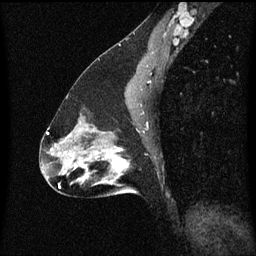
Breast MRI (dynamic contrast-enhanced), one sagittal slice; slice 34 of 60 in the series (ordered by position); dynamic contrast-enhanced series, image 2 of 3 at this slice position (ordered by acquisition); 1.5 T; TE 4.2 ms, TR 8.4 ms; 2 mm slice thickness; 256 × 256 image matrix. Patient: female, 47 years.
Outlined on this slice (semi-automatic segmentation, software-assisted and operator-edited):
- analysis volume of interest (the breast-tissue region the enhancement analysis was run in; not a lesion): box from (x=85, y=136) to (x=141, y=197) px
- tumour enhancement mask (voxels above the 70 % enhancement threshold inside the analysis volume of interest): (x=85, y=148)–(x=130, y=179)